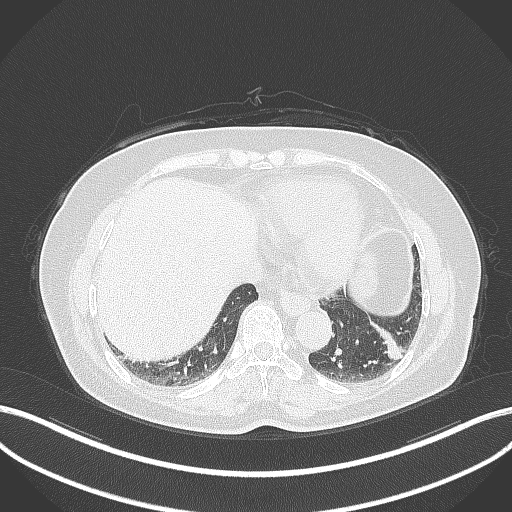
Chest CT, one axial slice. Position 105 of 311 along the scan axis. Reconstruction kernel B70f. Lung window (W 1500 / L -600 HU). 1 mm slice thickness. 512 × 512 image matrix, field of view 400 × 400 mm. Female patient, age 59 years. From the clinical record (not read from this slice): clinical TNM (as recorded): T2a N0 M0; histopathological grade: G2-3.
Outlined on this slice (rectangle marked by the reading radiologist):
- lung tumour (recorded histology: adenocarcinoma): bounding box (x1, y1, x2, y2) in pixels: (362, 314, 407, 367)